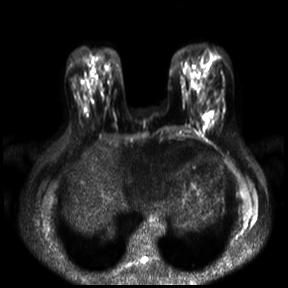
Breast MRI, one axial slice; slice 9 of 30 in the series (ordered by position); diffusion-weighted series; image 2 of 4 stored at this slice position (different b-values; order by instance number); 3 T; 4 mm slice thickness; 288 × 288 image matrix. Female patient.
Outlined on this slice (outlined manually by an expert reader):
- tumour on diffusion-weighted imaging: bounding box [x1, y1, x2, y2] px = [204, 112, 213, 123]